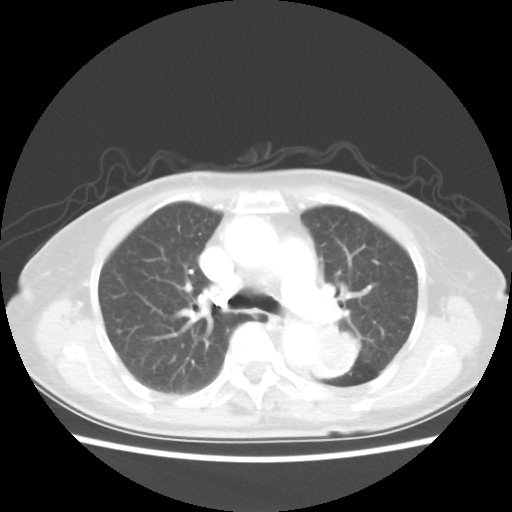
Chest CT, one axial slice; position 32 of 50 along the scan axis; reconstruction kernel STANDARD; 80 kVp; lung window (W 1500 / L -600 HU); 5 mm slice thickness; 512 × 512 image matrix, field of view 335 × 335 mm. Female patient, age 81 years. From the clinical record (not read from this slice): clinical TNM (as recorded): T2 N0 M1a.
Structures marked on this image (rectangle marked by the reading radiologist):
- lung tumour (recorded histology: squamous cell carcinoma): bounding box <310,319,358,383> (left, top, right, bottom; pixels)